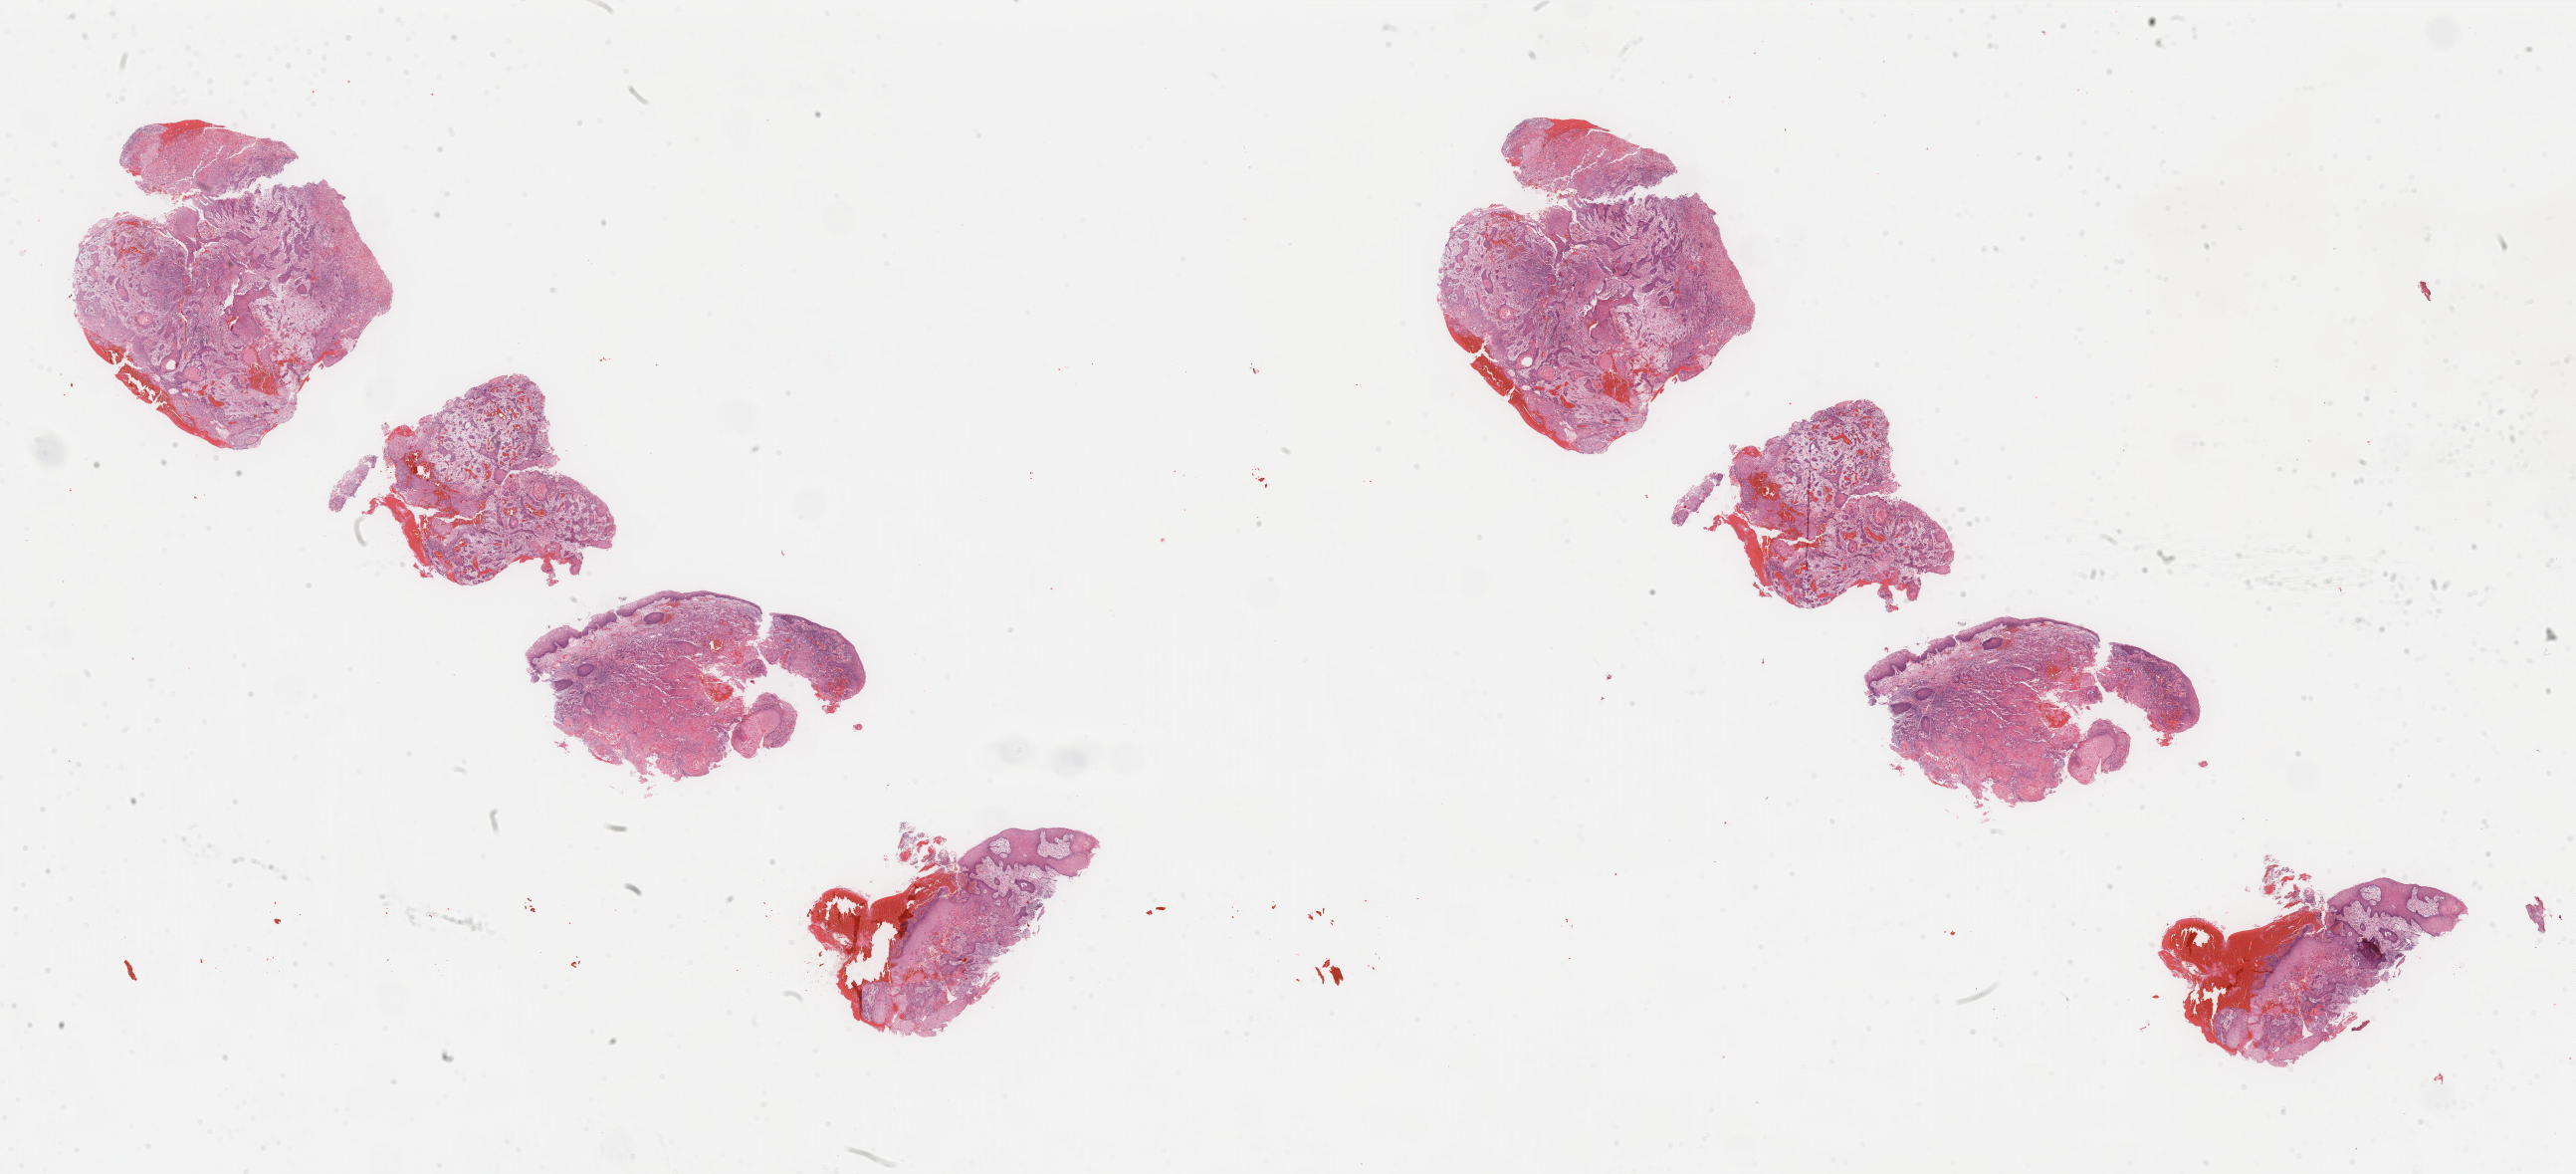
Digitized H&E tissue section (whole slide), whole scanned area (about 40.9 x 18.7 mm) shown as a low-resolution overview; formalin-fixed paraffin-embedded (FFPE) diagnostic section; sample: primary tumour, head and neck. Male, age 62 years at initial diagnosis. Histologic grade: G2 (moderately differentiated).
* histologic diagnosis: Squamous cell carcinoma, keratinizing, NOS (larynx, NOS)